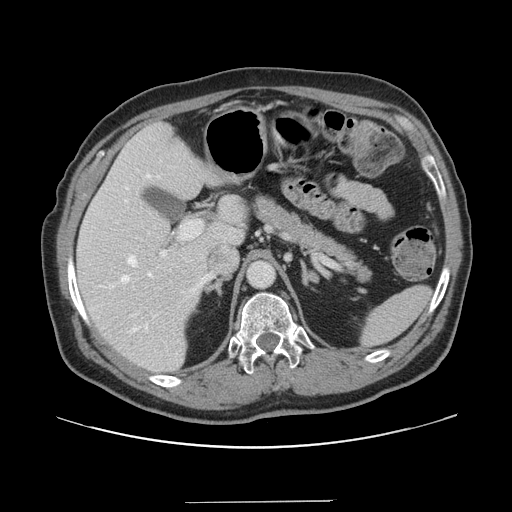
Contrast-enhanced abdominal CT, one axial slice. Slice 95 of 151 in the series (ordered by position). 120 kVp. Intravenous contrast given. Soft-tissue window (W 400 / L 40 HU). 2.5 mm slice thickness. 512 × 512 image matrix. Male patient, age 63 years. Case-level facts recorded for this patient, not image findings: diagnosis: colorectal cancer liver metastases, imaged before liver resection; multiple liver metastases: no; largest metastasis: 2.1 cm; disease in both lobes: no.
Outlined on this slice (manually delineated by an expert):
- hepatic veins: bounding box <121,174,212,333> (left, top, right, bottom; pixels)
- liver: <77,124,247,373>
- planned liver remnant (the part of the liver to remain after resection): <77,124,246,373>
- portal vein (with intrahepatic branches): <160,220,202,257>